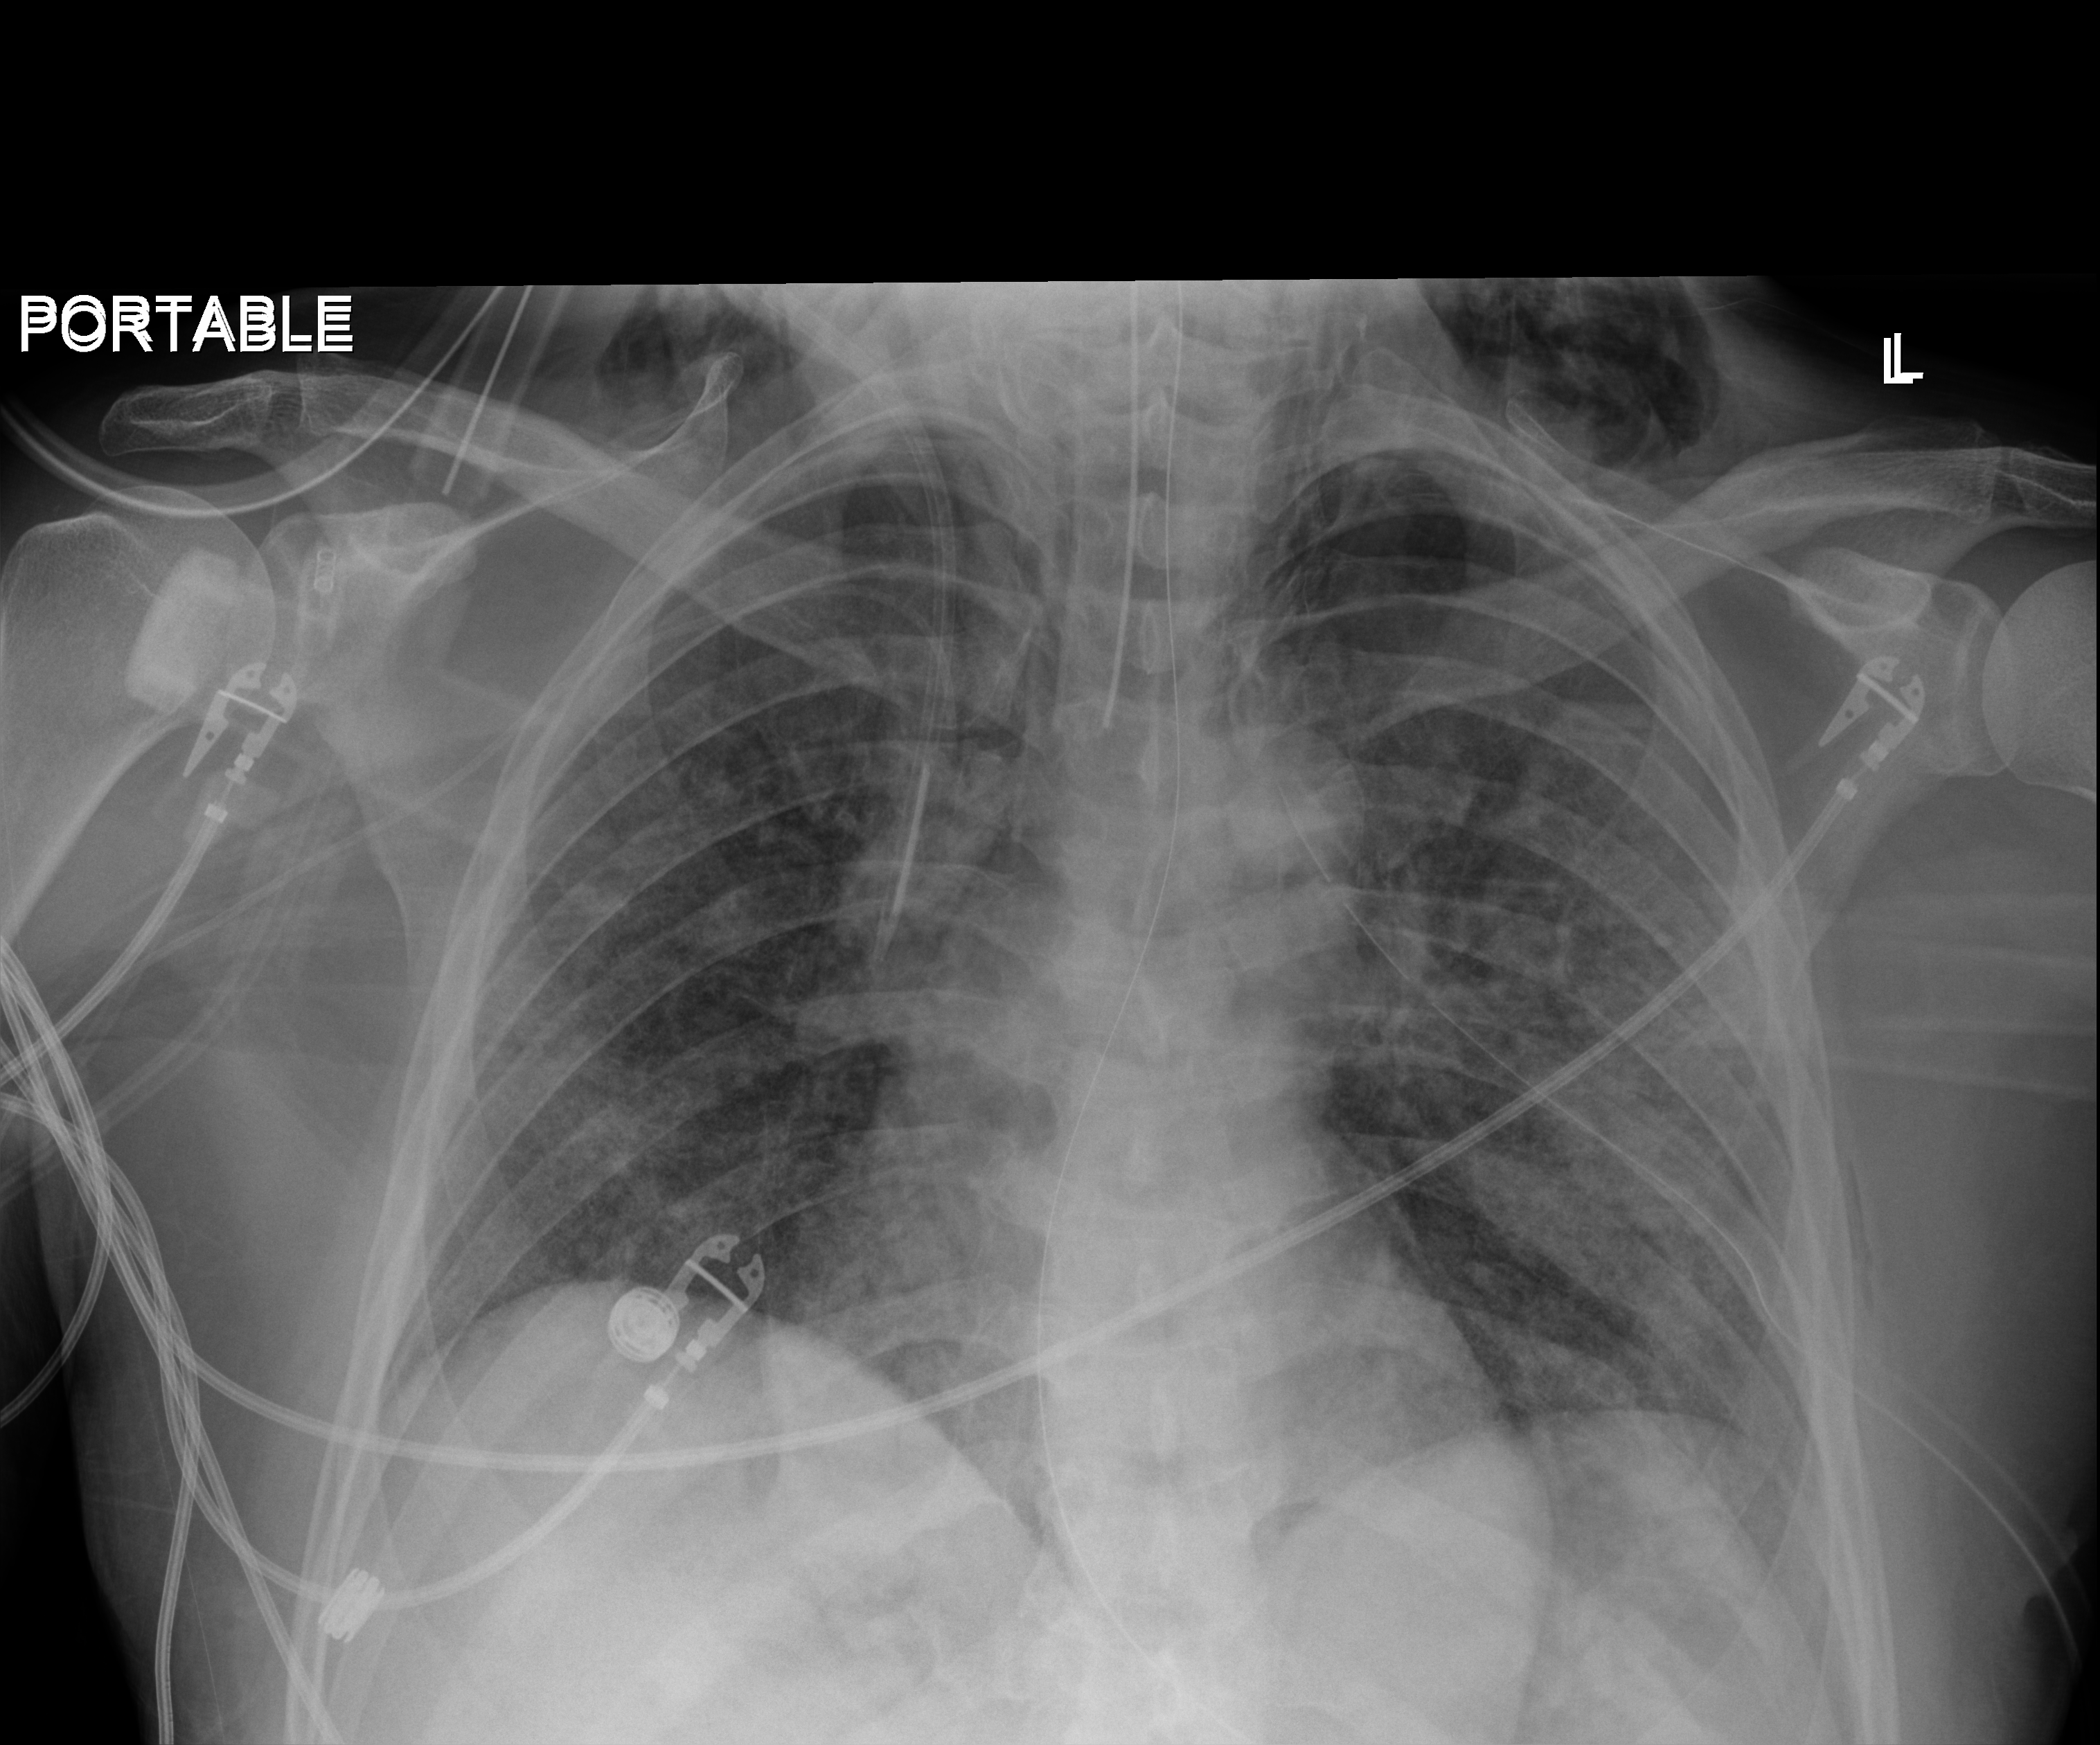
Chest X-ray (portable); anteroposterior (AP) projection. Male patient hospitalised with COVID-19, age 18–59 years.
Admission-level facts for this patient (not findings on this image; timing relative to this image not recorded): chronic kidney disease (admission record): no.